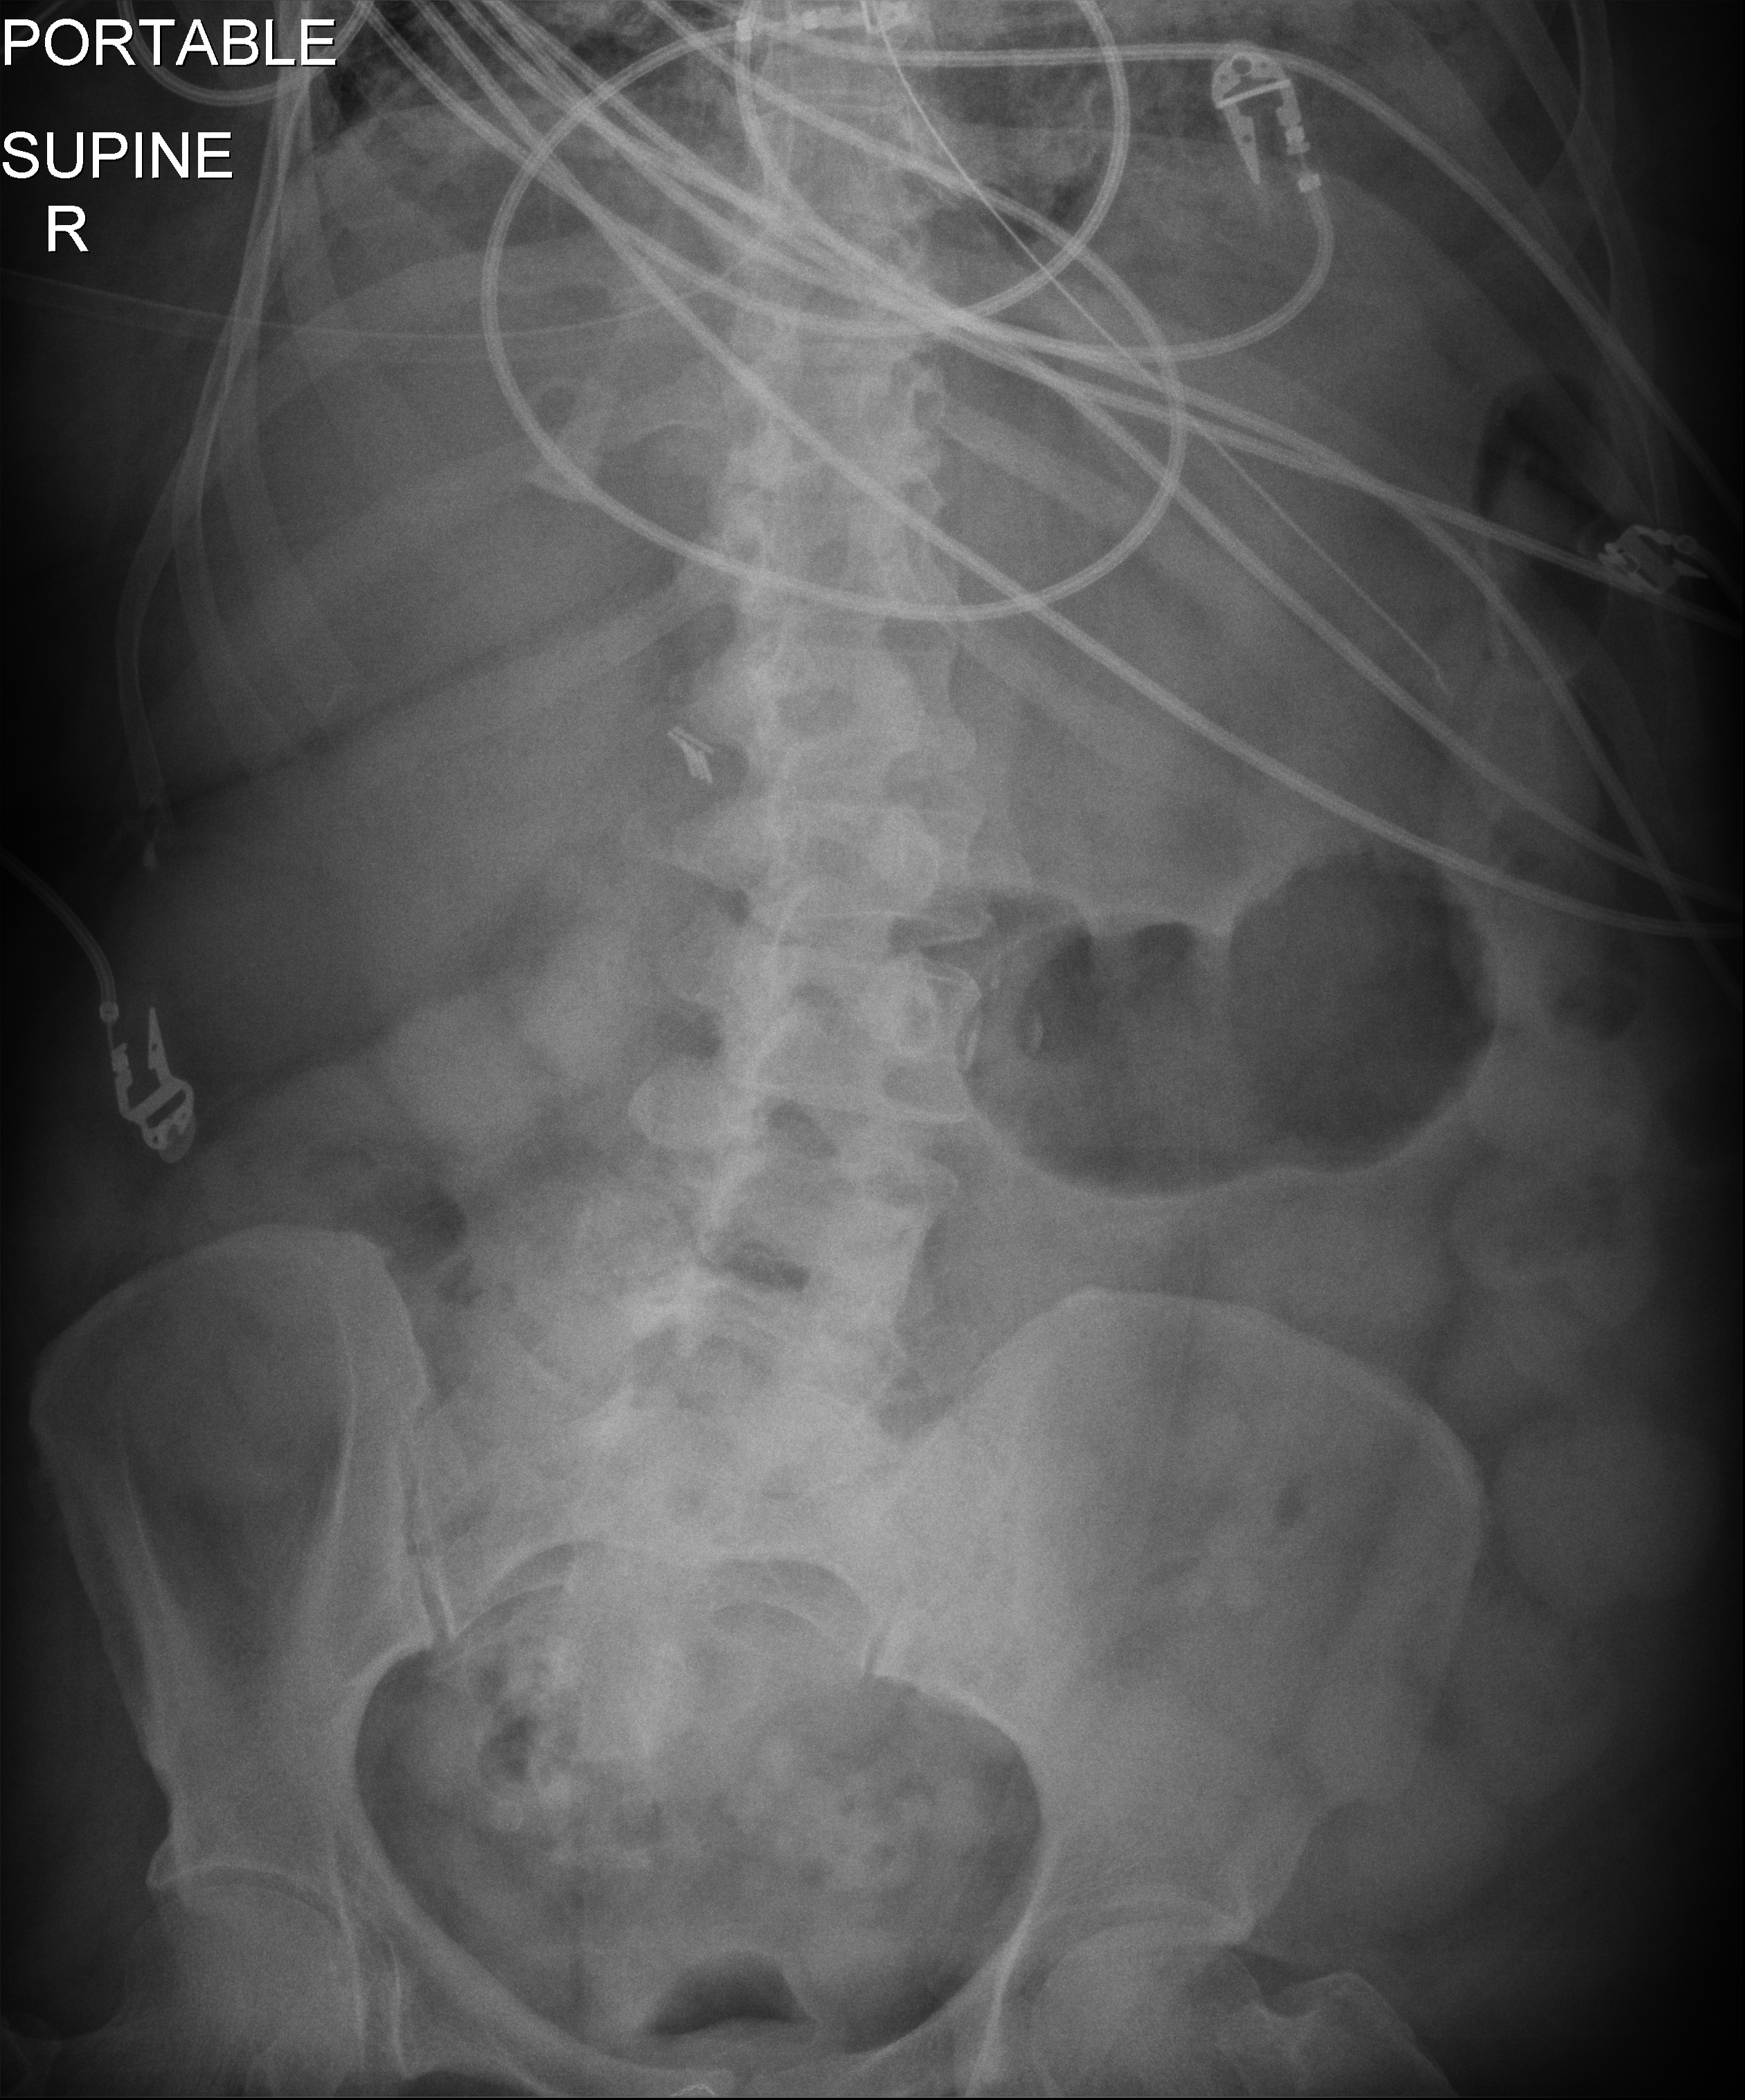
Bedside abdomen radiograph (digital radiography); anteroposterior (AP) projection. Female patient hospitalised with COVID-19, age 60–74 years.
From the hospital-stay record, not from the radiograph (when in the stay this image was taken is not recorded): mechanically ventilated during this hospital stay: yes; admitted to intensive care during this hospital stay: yes.